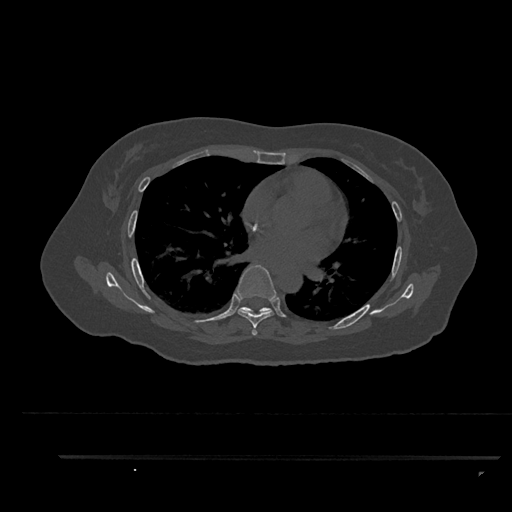
CT including the spine, one axial slice; slice 544 of 797 in the series (ordered by position); reconstruction kernel Br40s/3; 120 kVp; bone window (W 1800 / L 400 HU); 512 × 512 image matrix, field of view 408 × 408 mm. Female patient, age 44 years. From the clinical record (not read from this slice): primary cancer: renal.
Structures marked on this image (semi-automatically segmented with operator editing):
- T6 vertebra: box from (x=235, y=265) to (x=276, y=336) px
- T7 vertebra: (x=242, y=307)–(x=272, y=315)